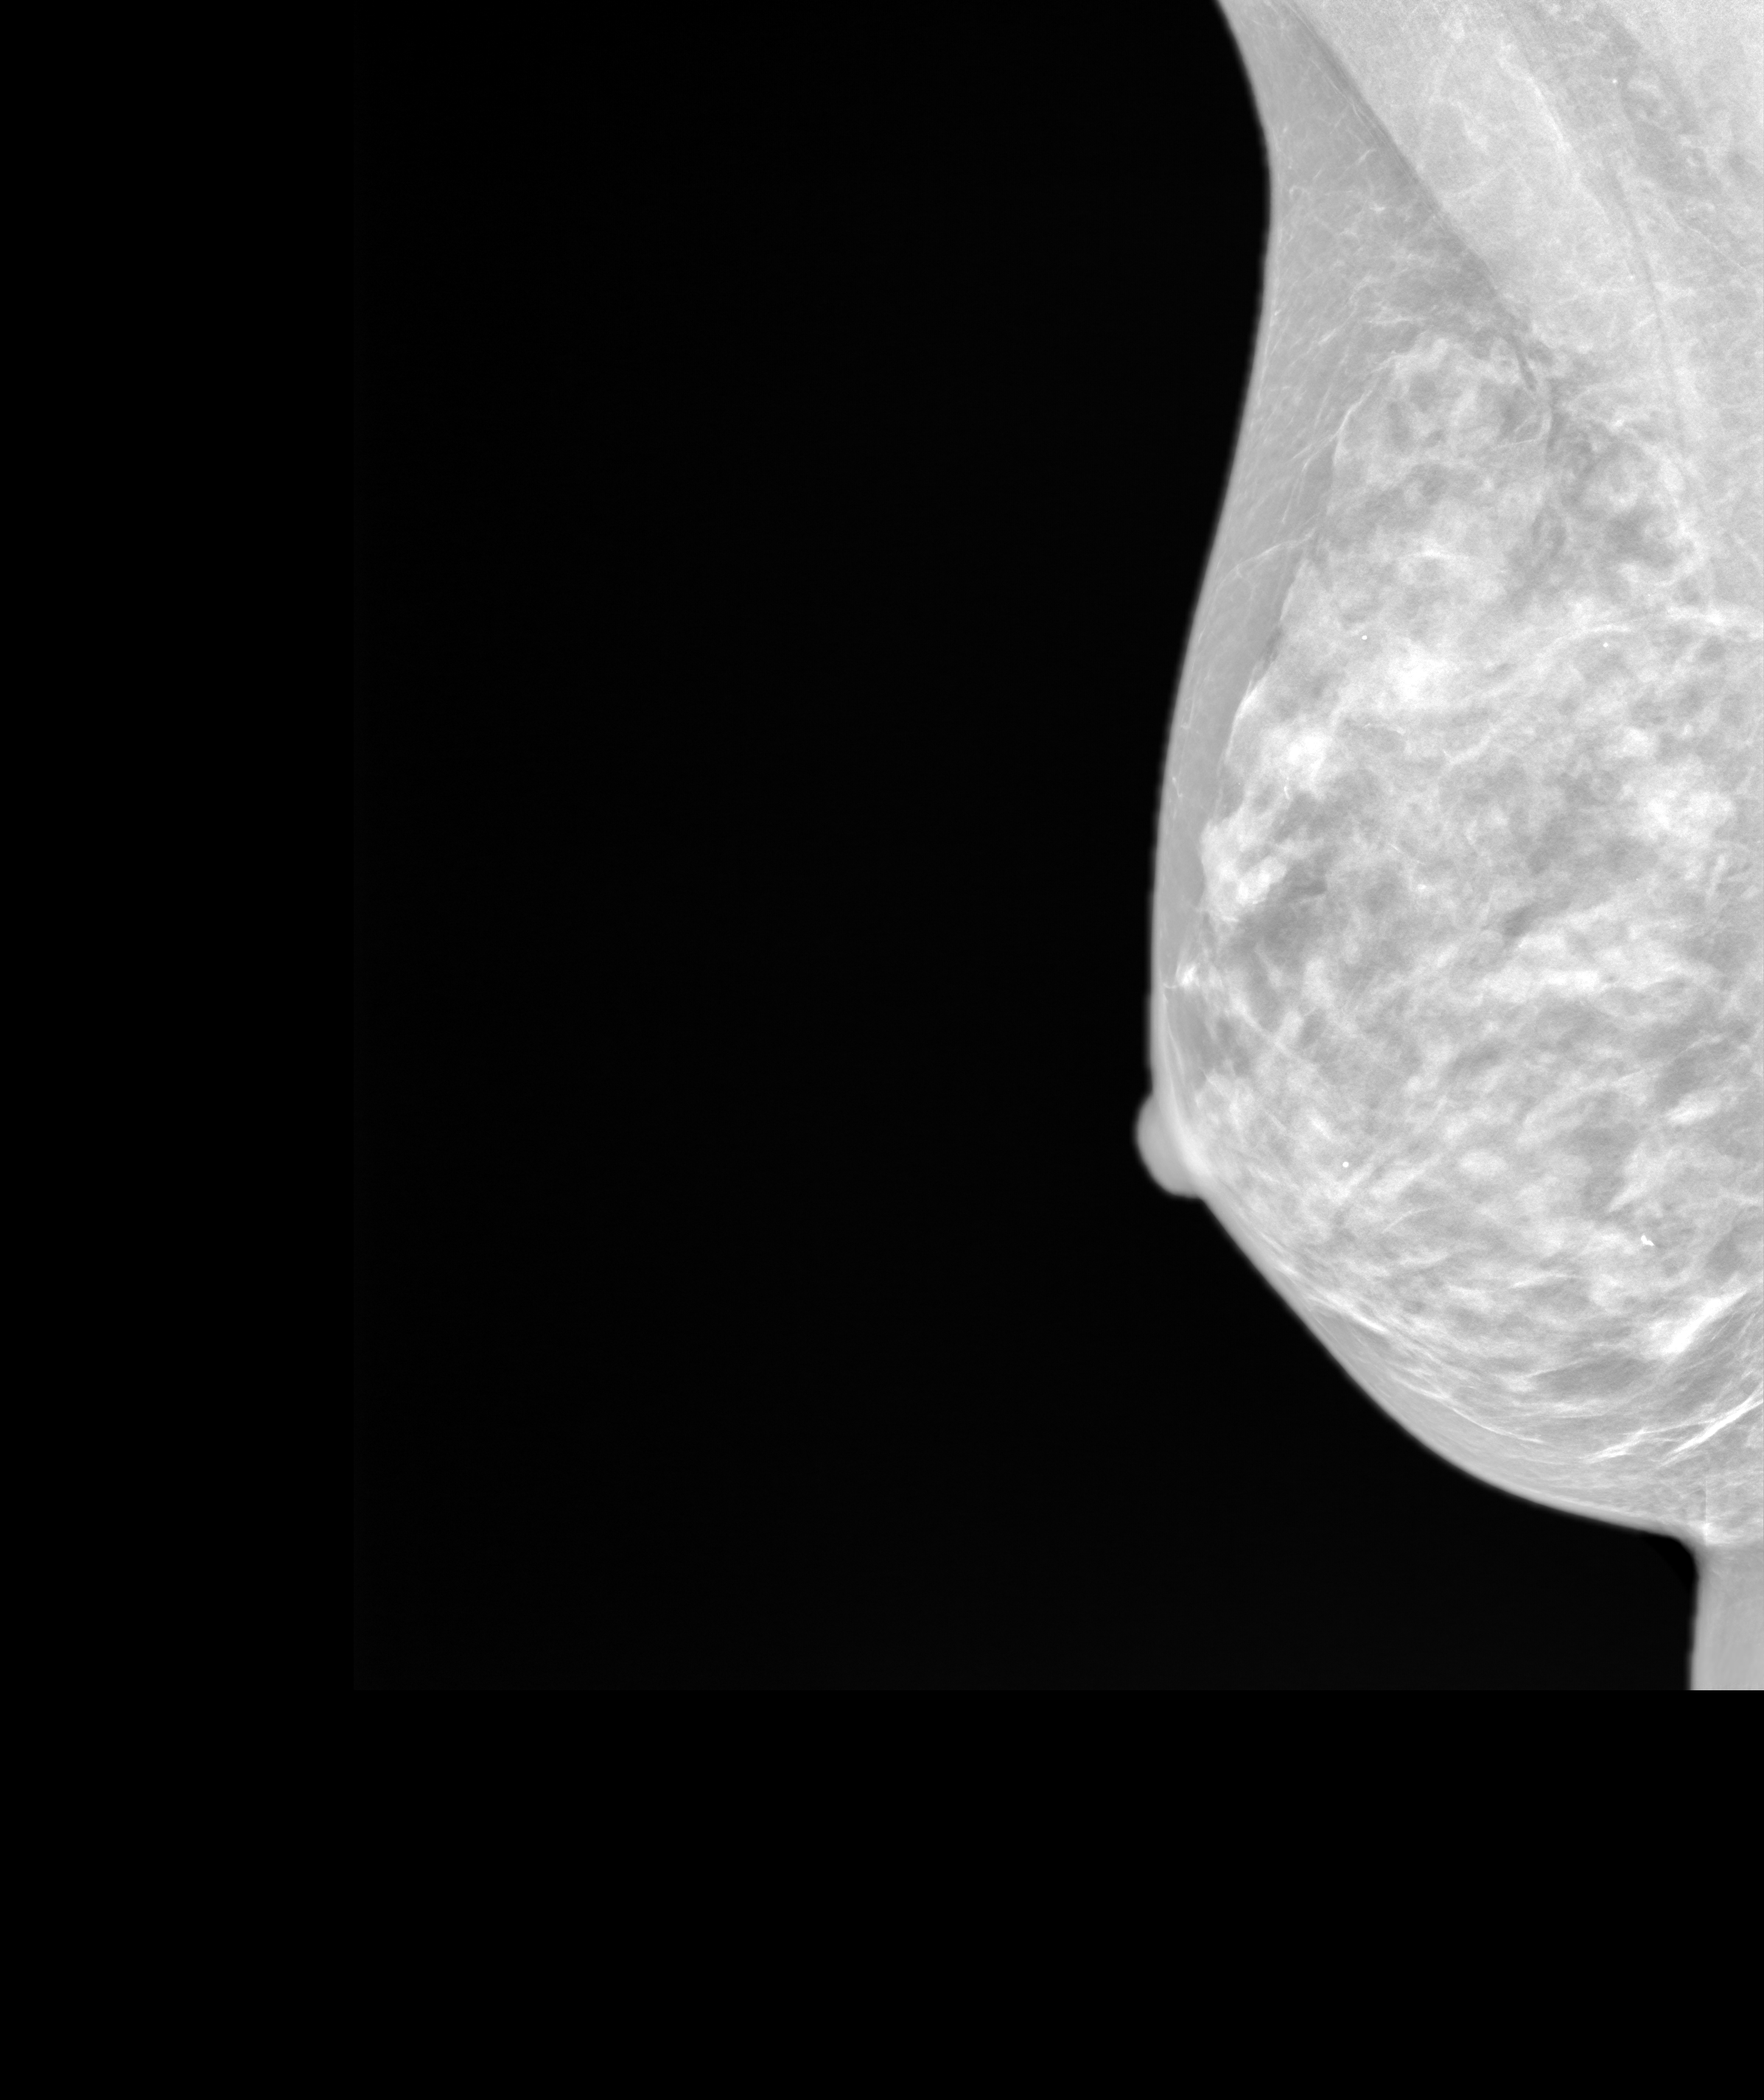
Annual screening mammography examination, system: SenoIris_1SP1.2(425). Female patient, age 73 years.
Image type: synthesized 2-D view from tomosynthesis. Breast: right. Projection: medio-lateral oblique projection. Breast density at the screening exam (both breasts): extremely dense (BI-RADS density category d). Final BI-RADS category for the screening round (tomosynthesis exam, both breasts): category 1. Recall: no recall after this screen.